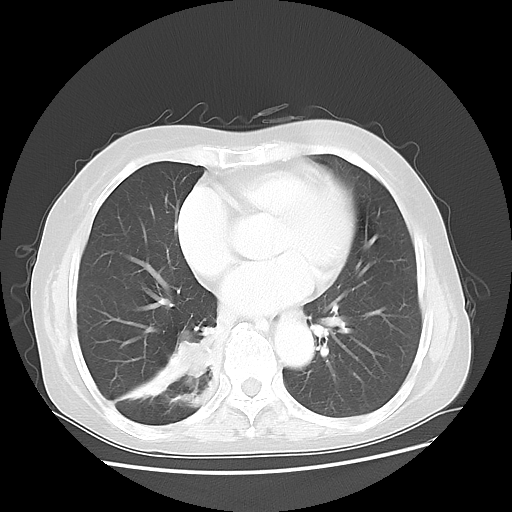
Chest CT, one axial slice. Position 18 of 47 along the scan axis. Reconstruction kernel LUNG. Lung window (W 1500 / L -600 HU). 5 mm slice thickness. 512 × 512 image matrix, field of view 360 × 360 mm. Patient: female, 63 years. Case-level facts recorded for this patient, not image findings: clinical TNM (as recorded): T2 N3 M1b.
Outlined on this slice (rectangle marked by the reading radiologist):
- lung tumour (recorded histology: small cell carcinoma): bounding box (x1, y1, x2, y2) in pixels: (162, 318, 219, 392)